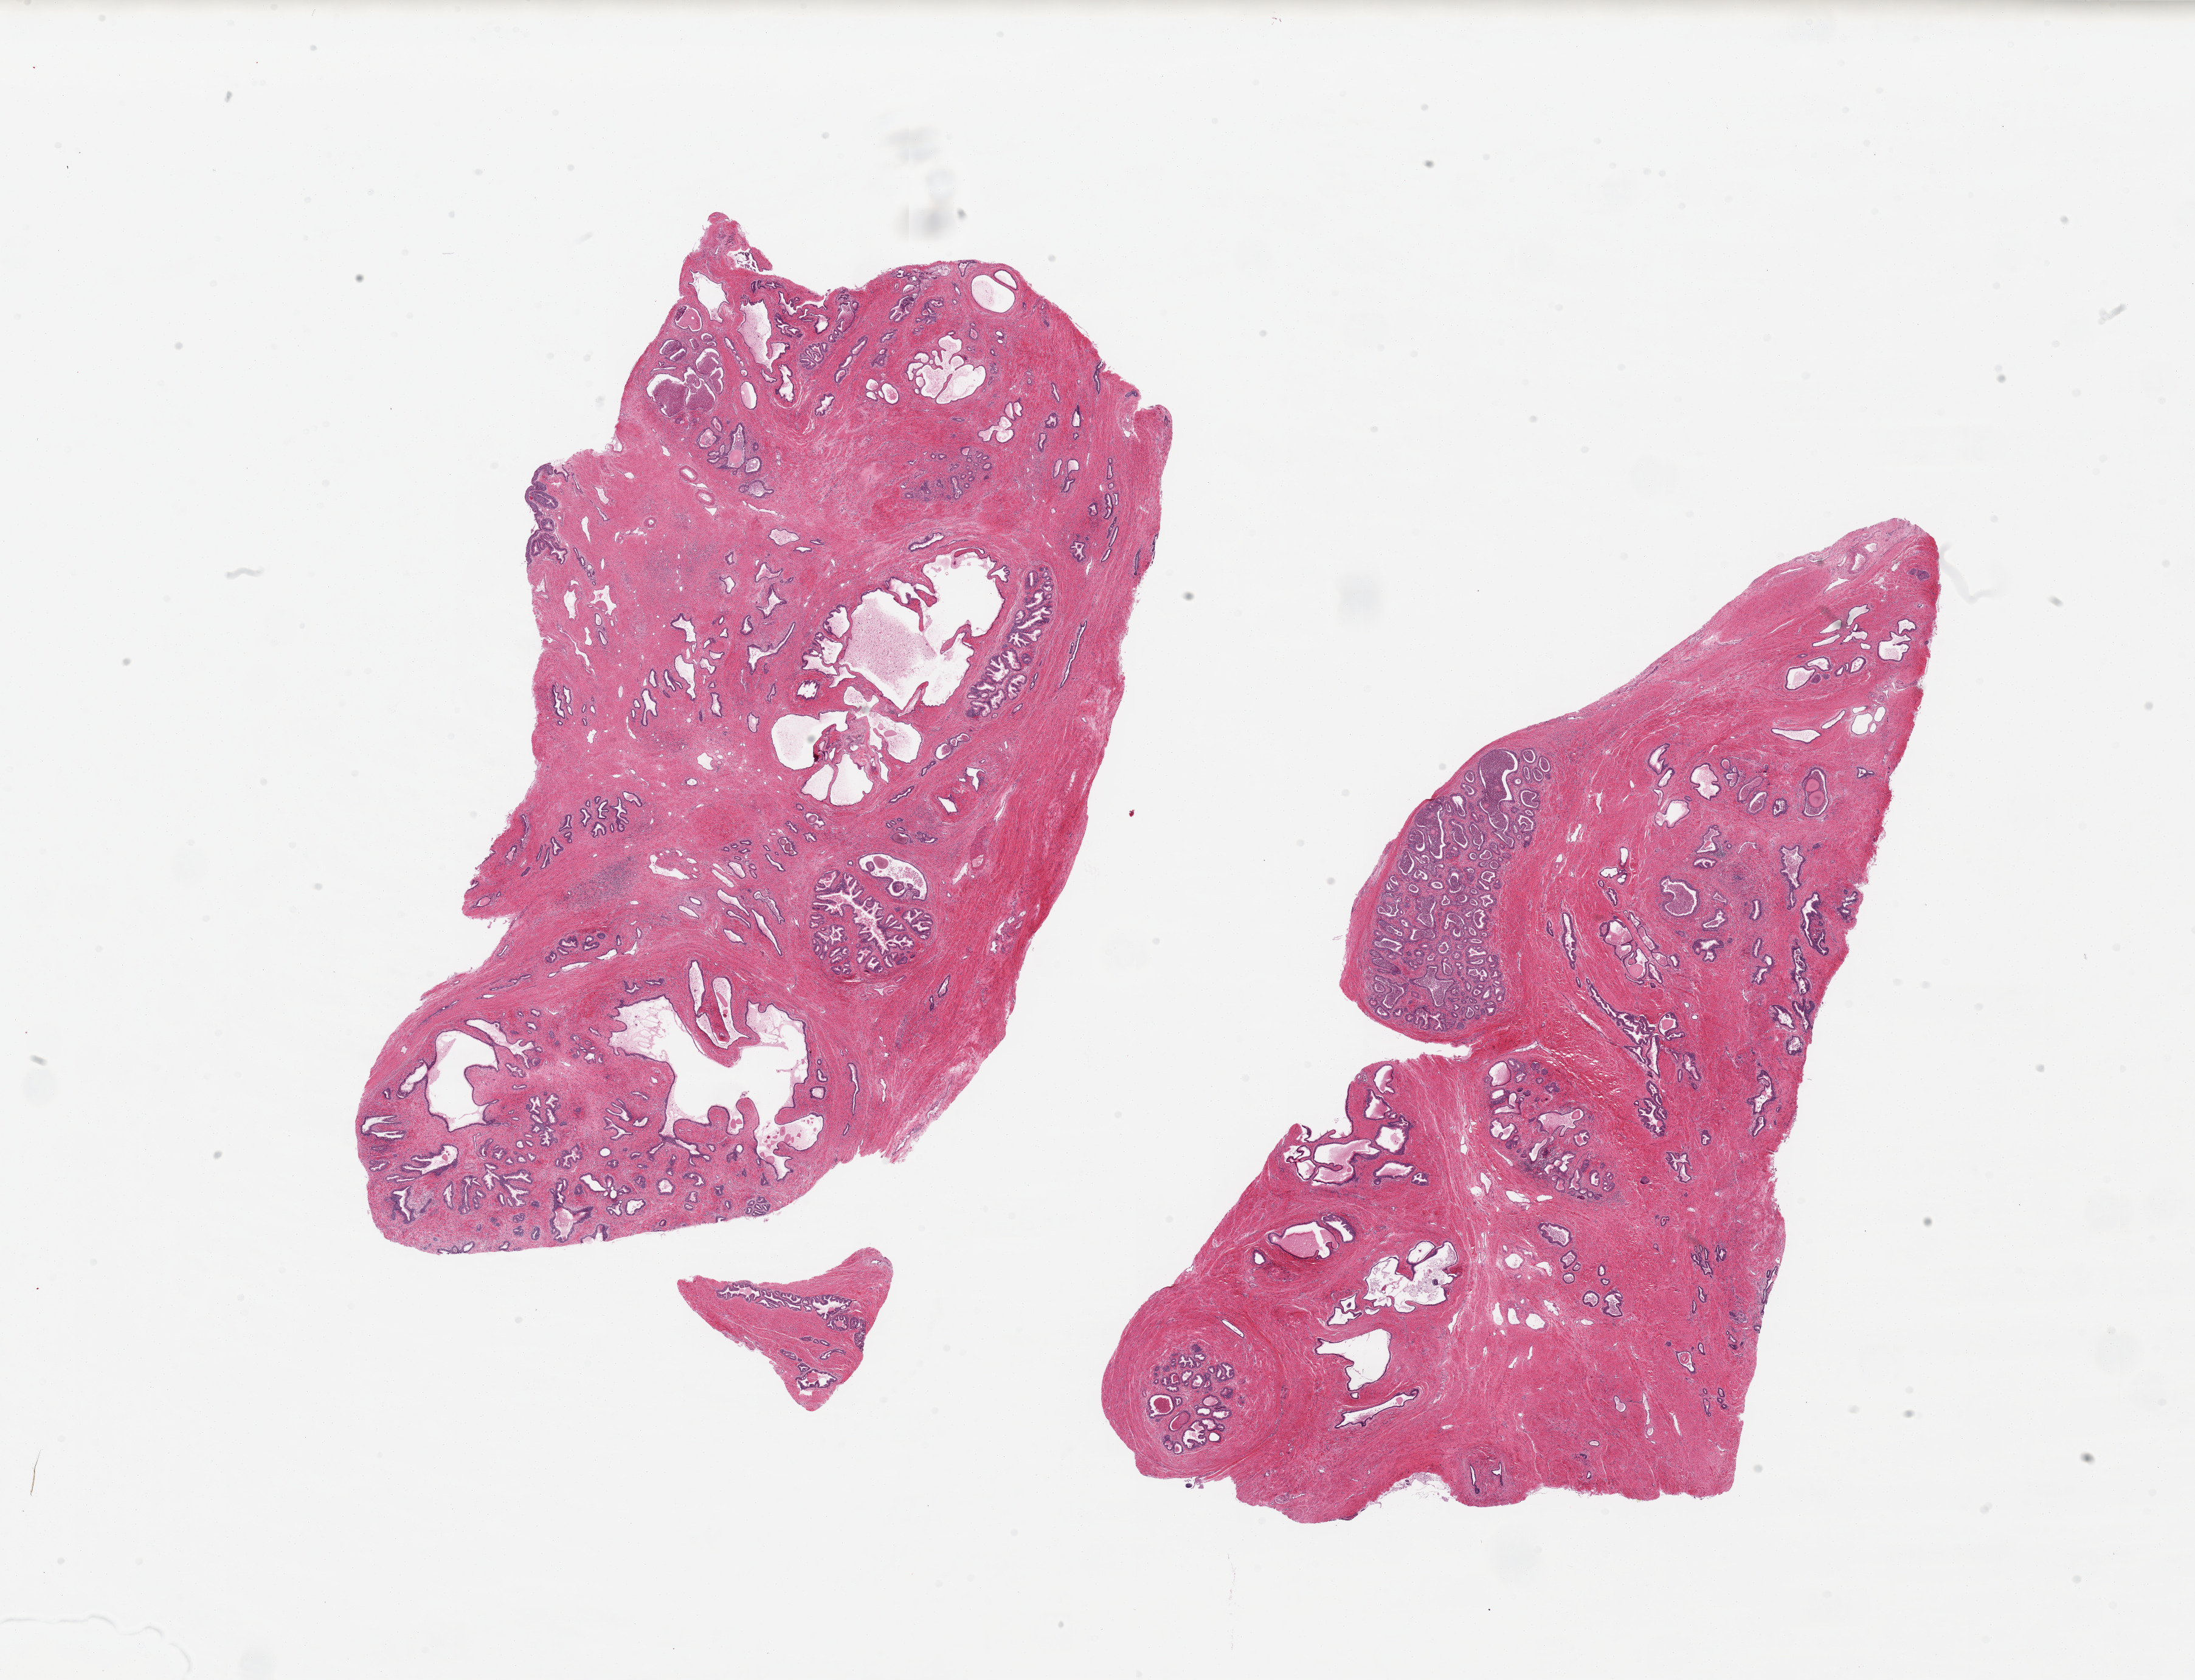
Whole-slide image, haematoxylin and eosin stain — low-resolution overview of the scanned area, about 28.5 x 21.9 mm (from a 20x scan), PAXgene-fixed paraffin-embedded (PFPE) section, section of prostate (target tissue), tissue donor sample. Male donor.
Reviewer comment on this tissue sample: 2 pieces, glandular hyperplastic pattern, patchy acute prostatis.